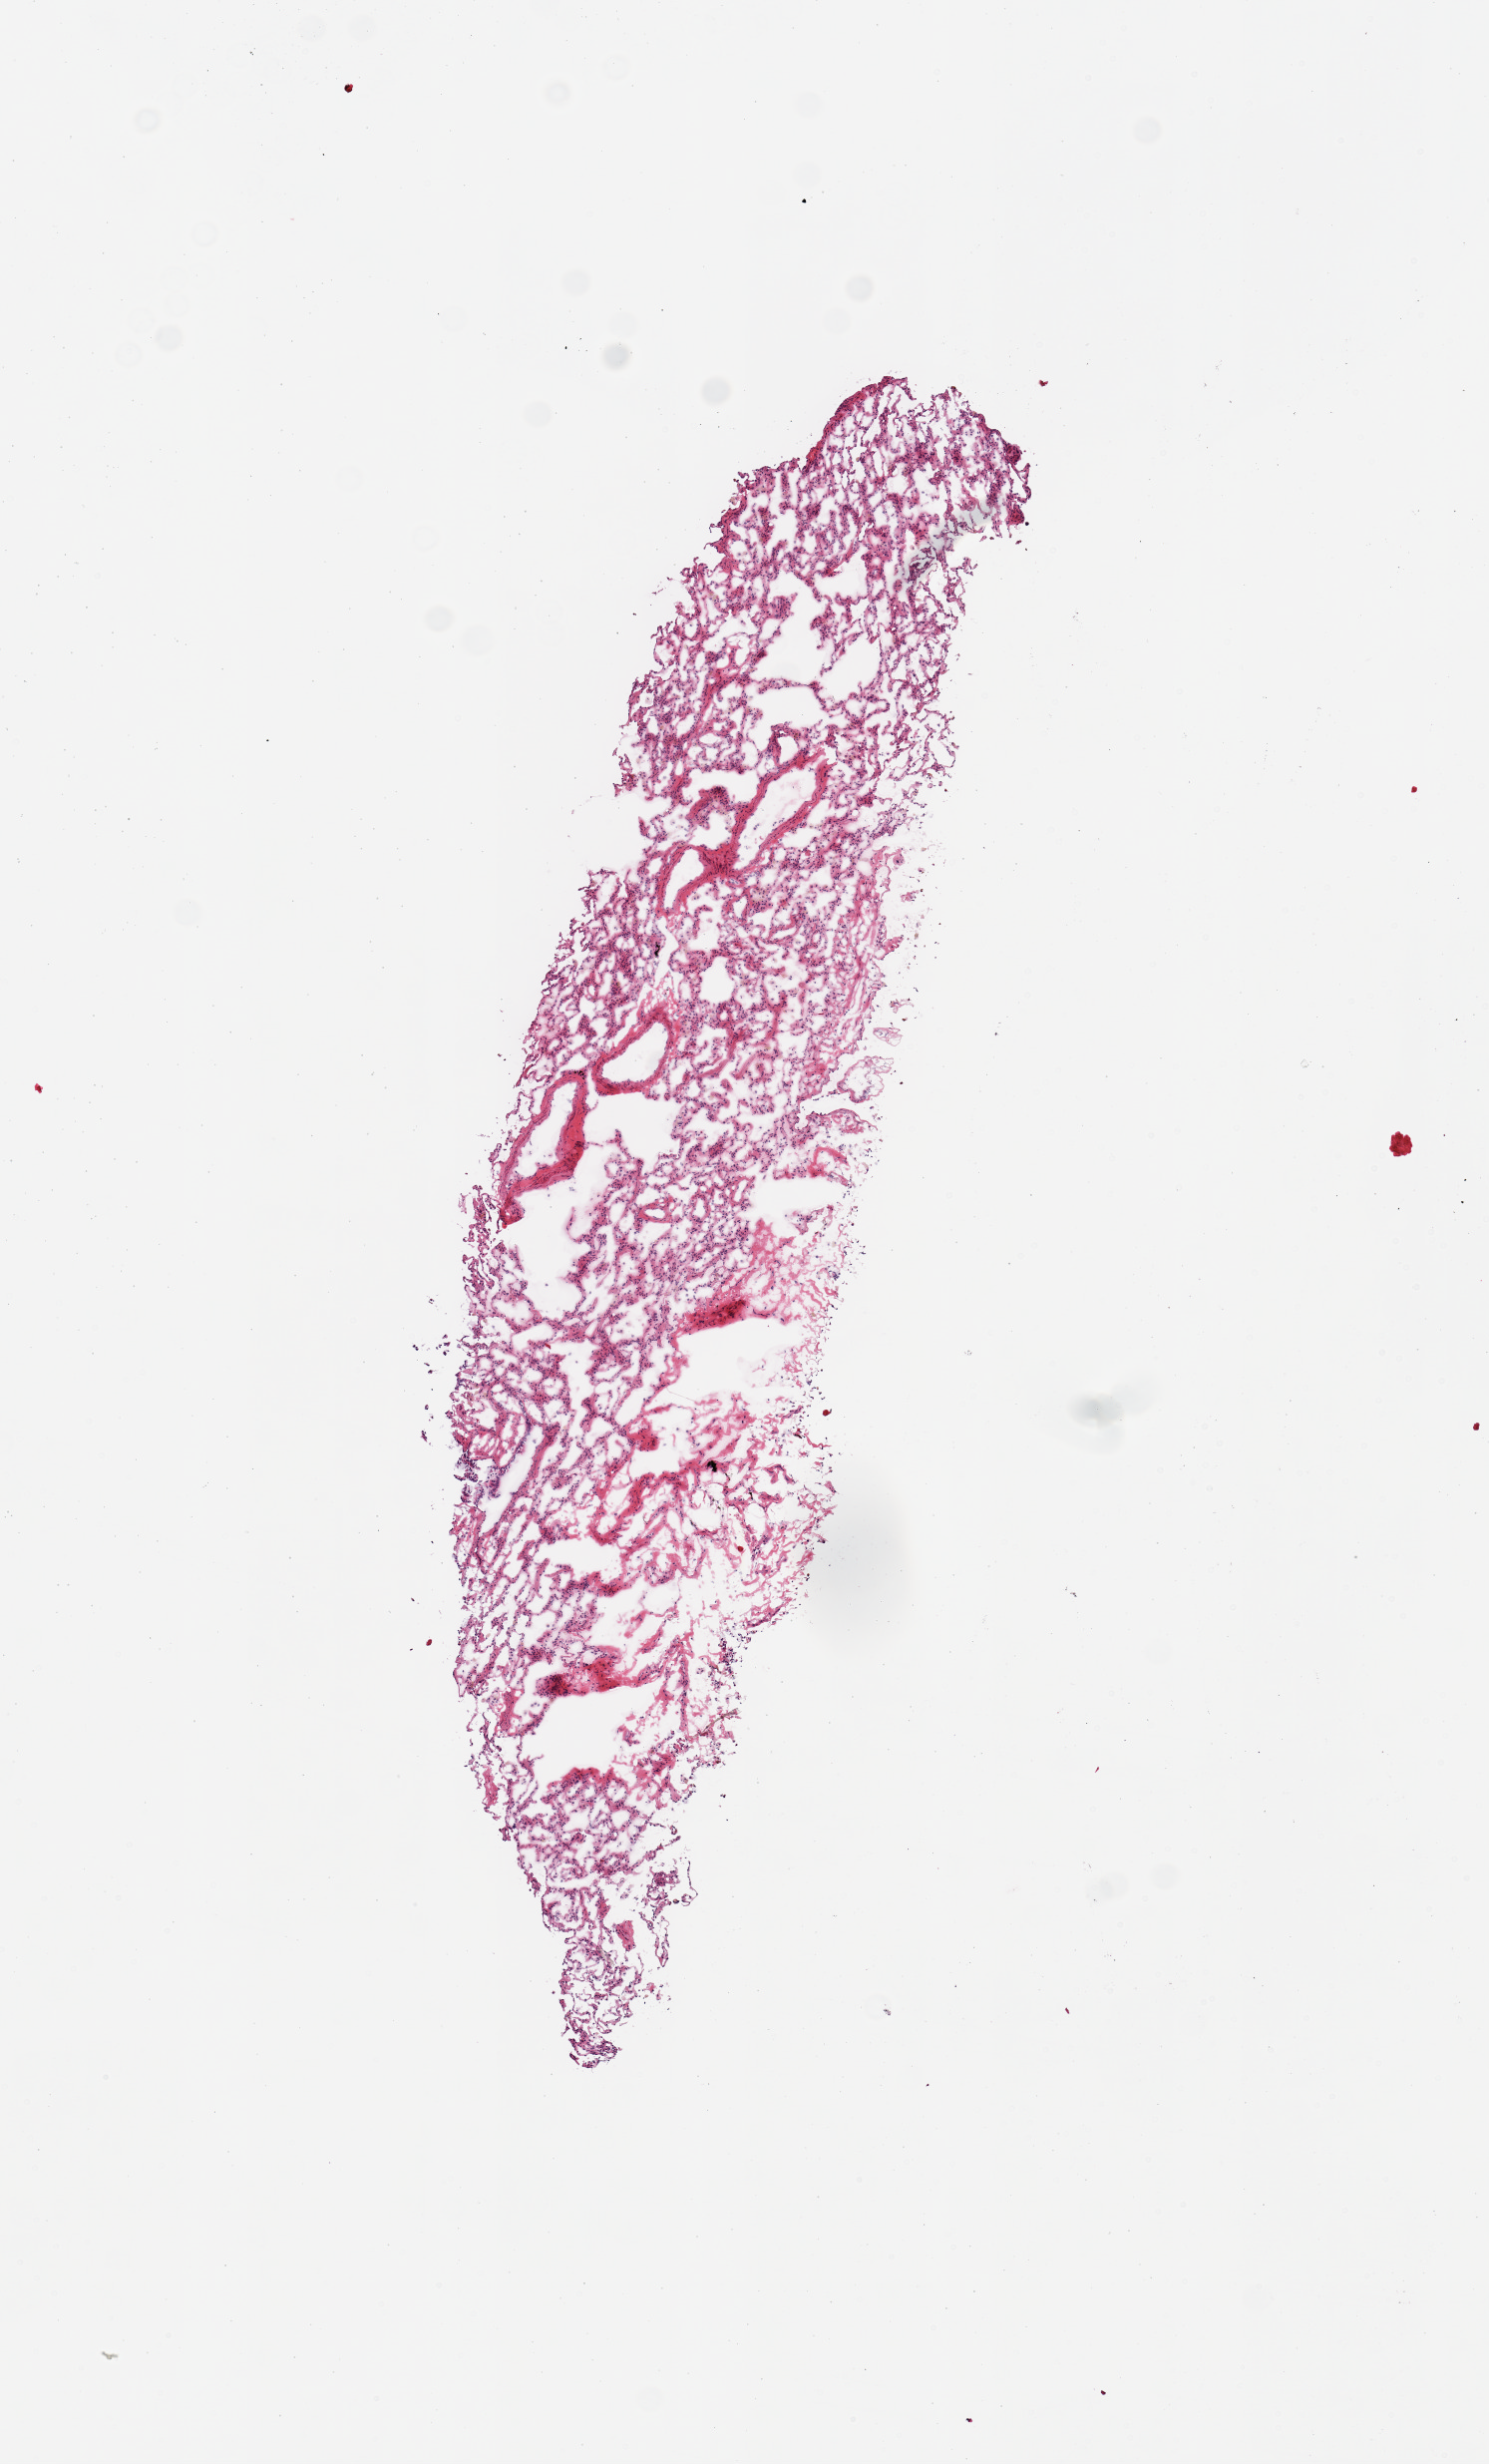
Haematoxylin and eosin whole-slide image, brightfield — whole scanned area (about 5.9 x 9.8 mm, from a 20x scan) shown as a low-resolution overview.
Specimen: frozen section (dry ice); section of lung (target tissue); donor tissue sample.